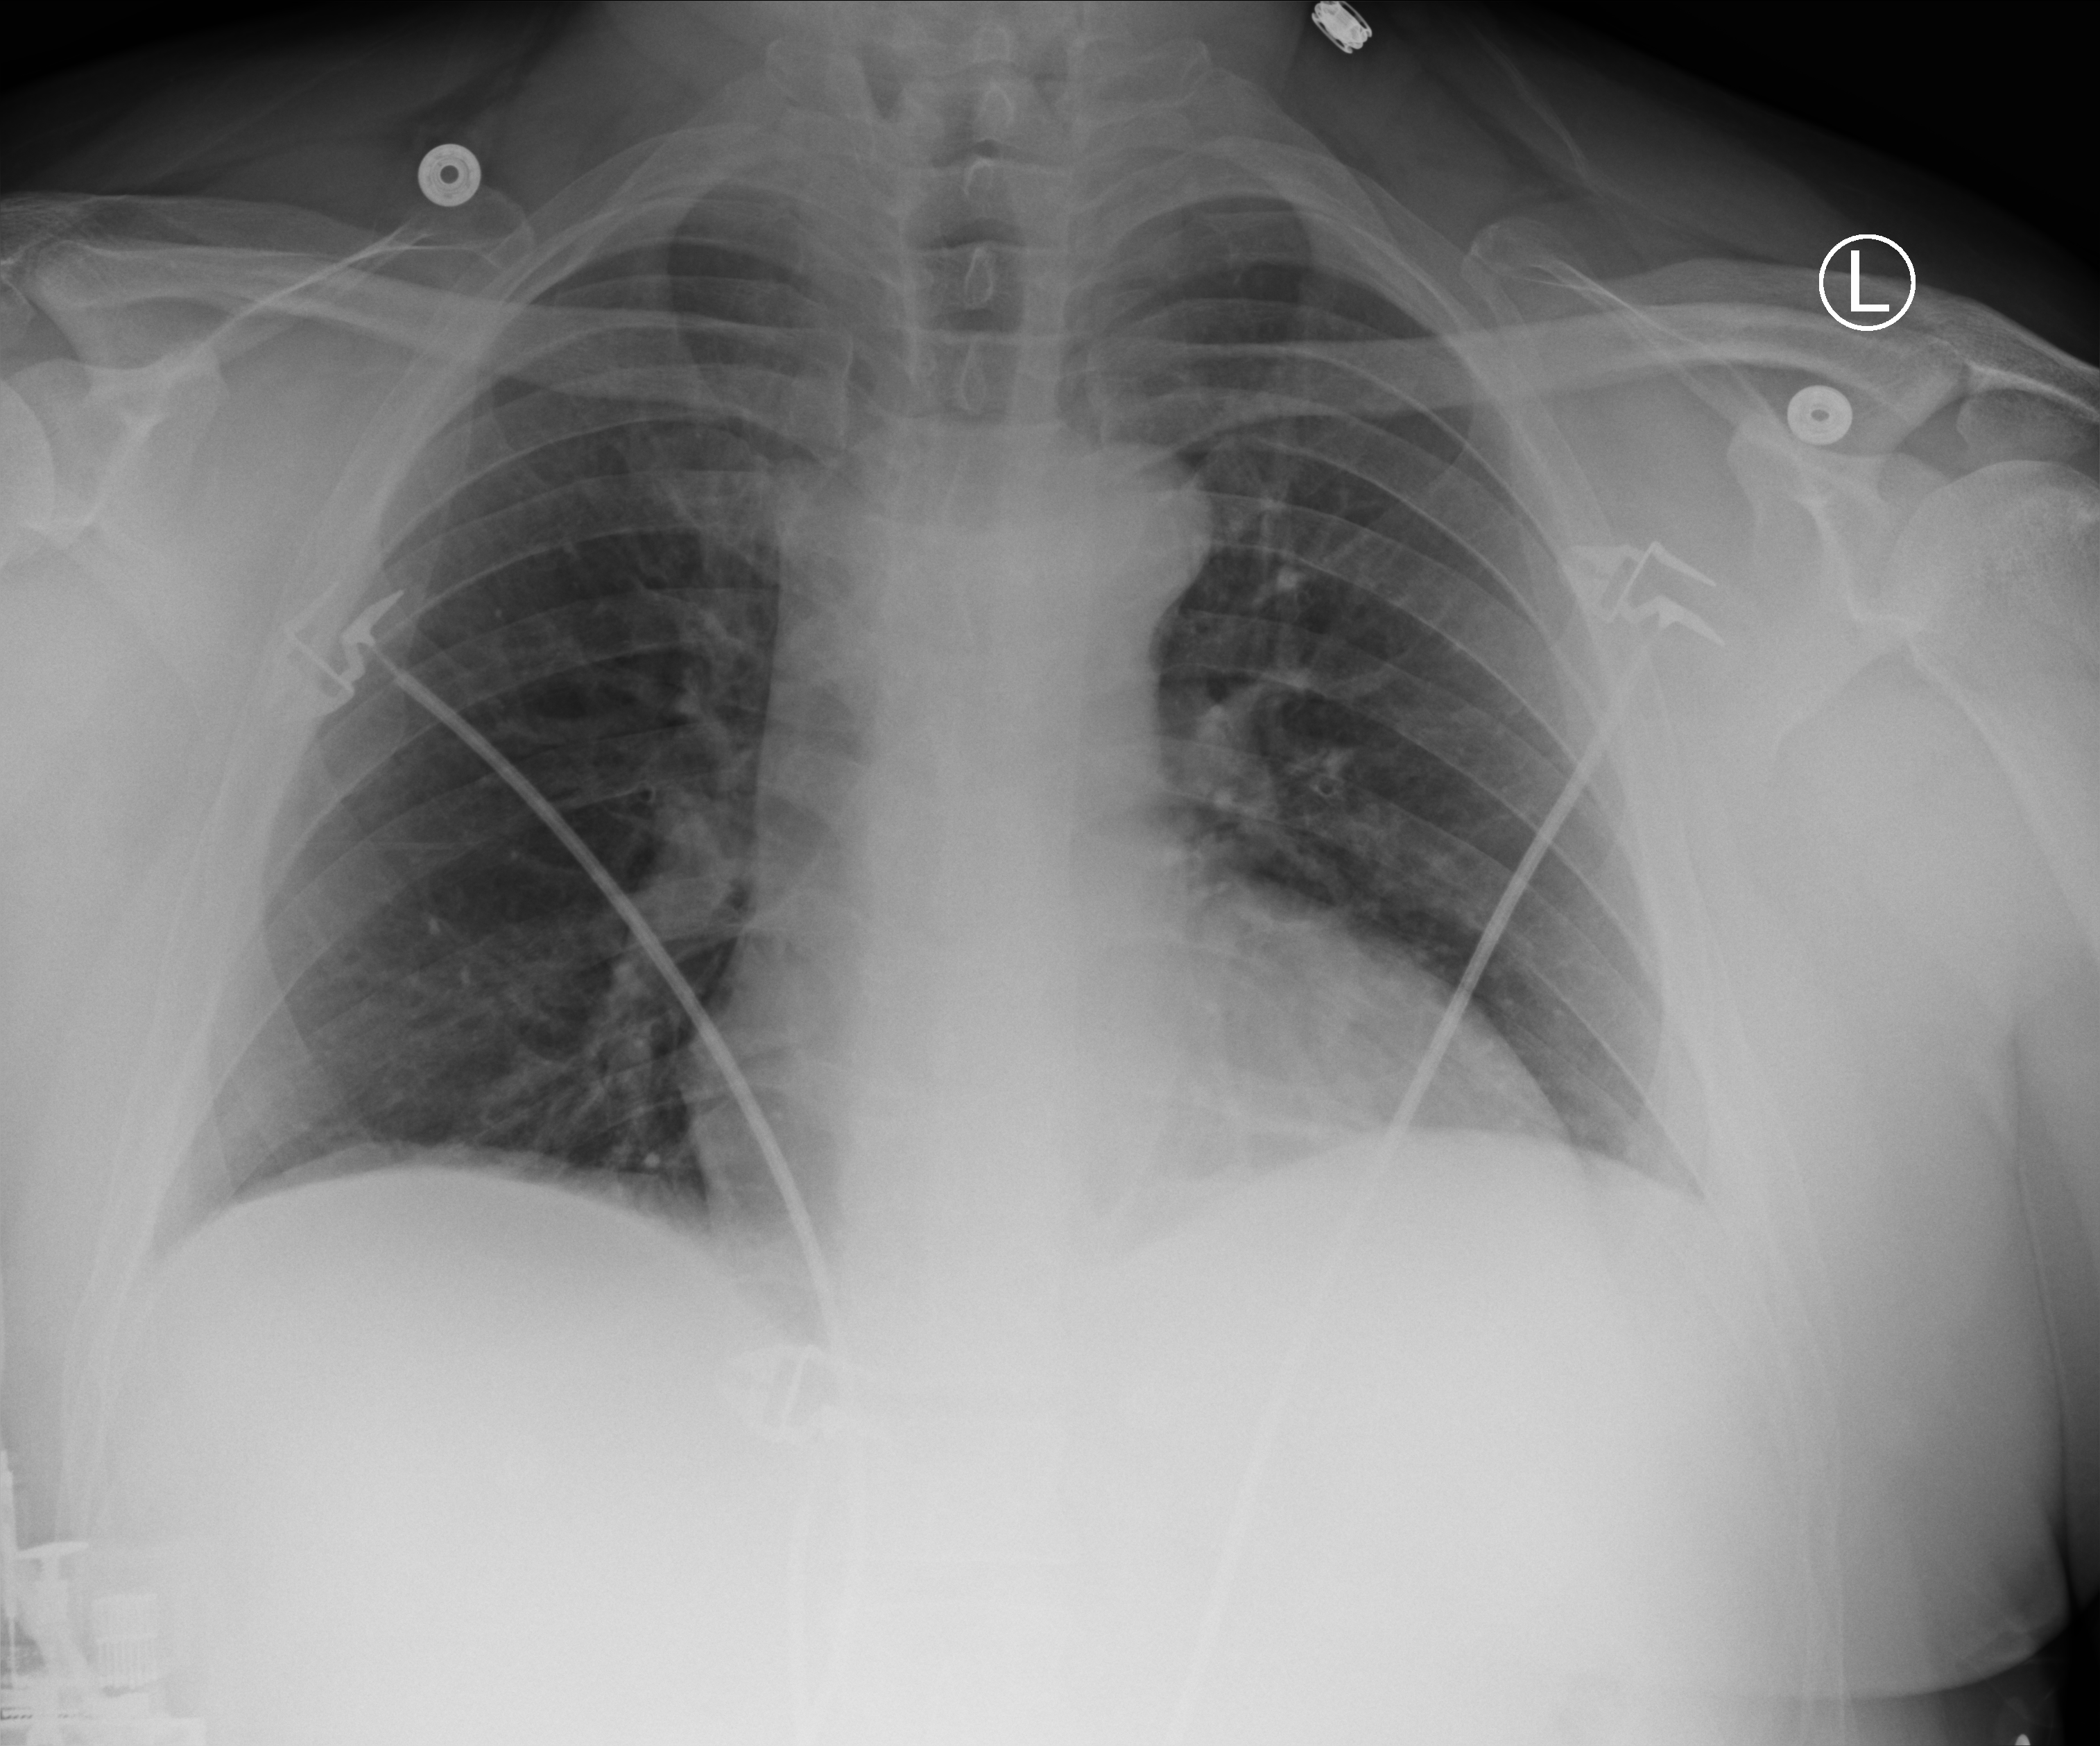
Bedside chest radiograph (computed radiography), anteroposterior (AP) projection. Patient hospitalised with COVID-19; male, aged 18–59 years.
Hospital-stay facts (about this admission, not read from this image; timing relative to this image not recorded): other chronic lung disease (admission record): yes.